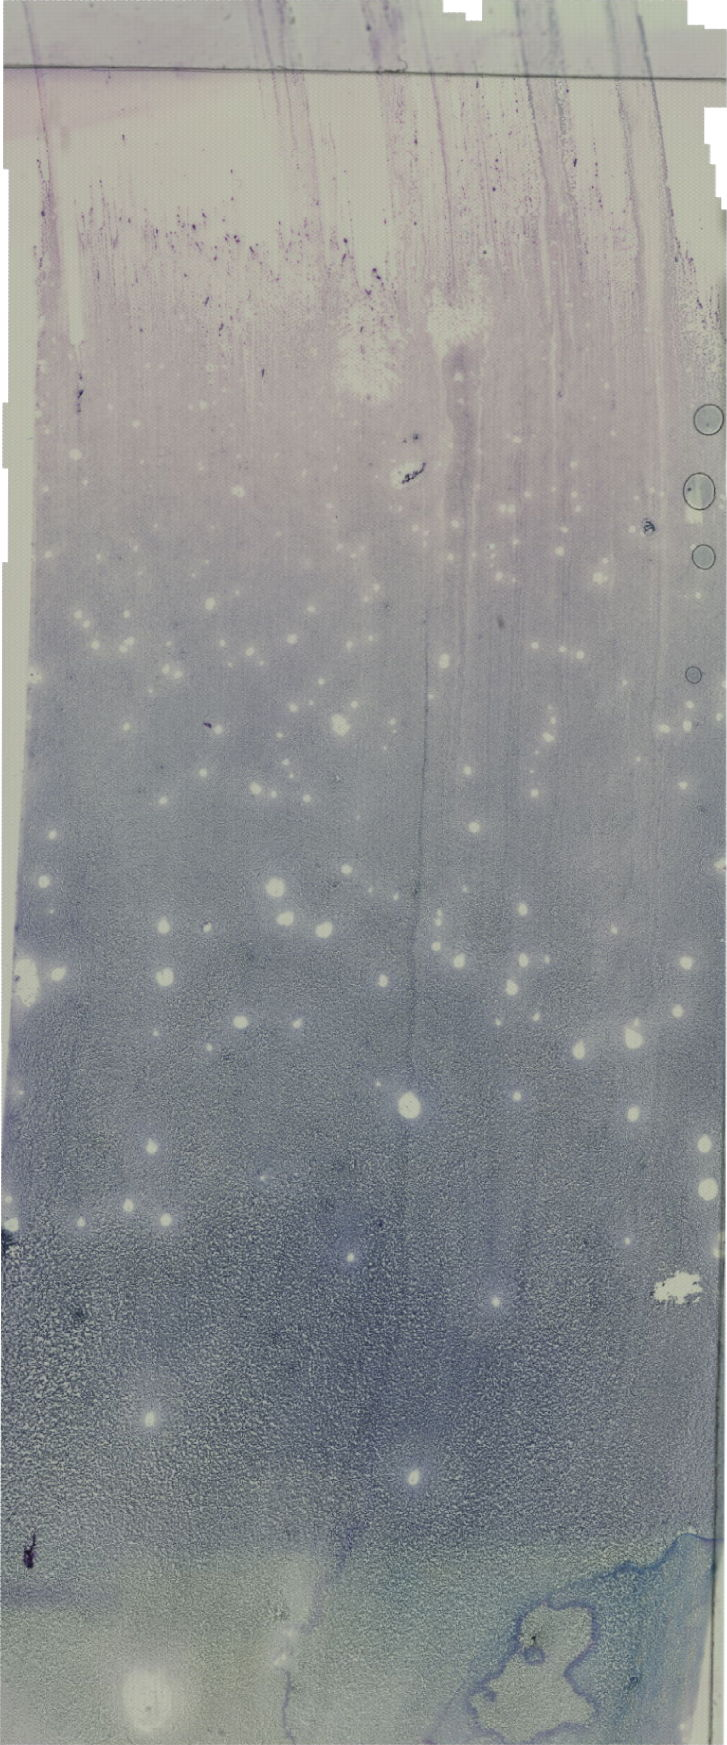
Whole-slide image of a May-Grünwald-Giemsa (MGG)-stained bone marrow aspirate smear, low-resolution overview of the scanned area, about 20.6 x 49.5 mm. Male patient.
Diagnosis: B Acute Lymphoblastic Leukemia.